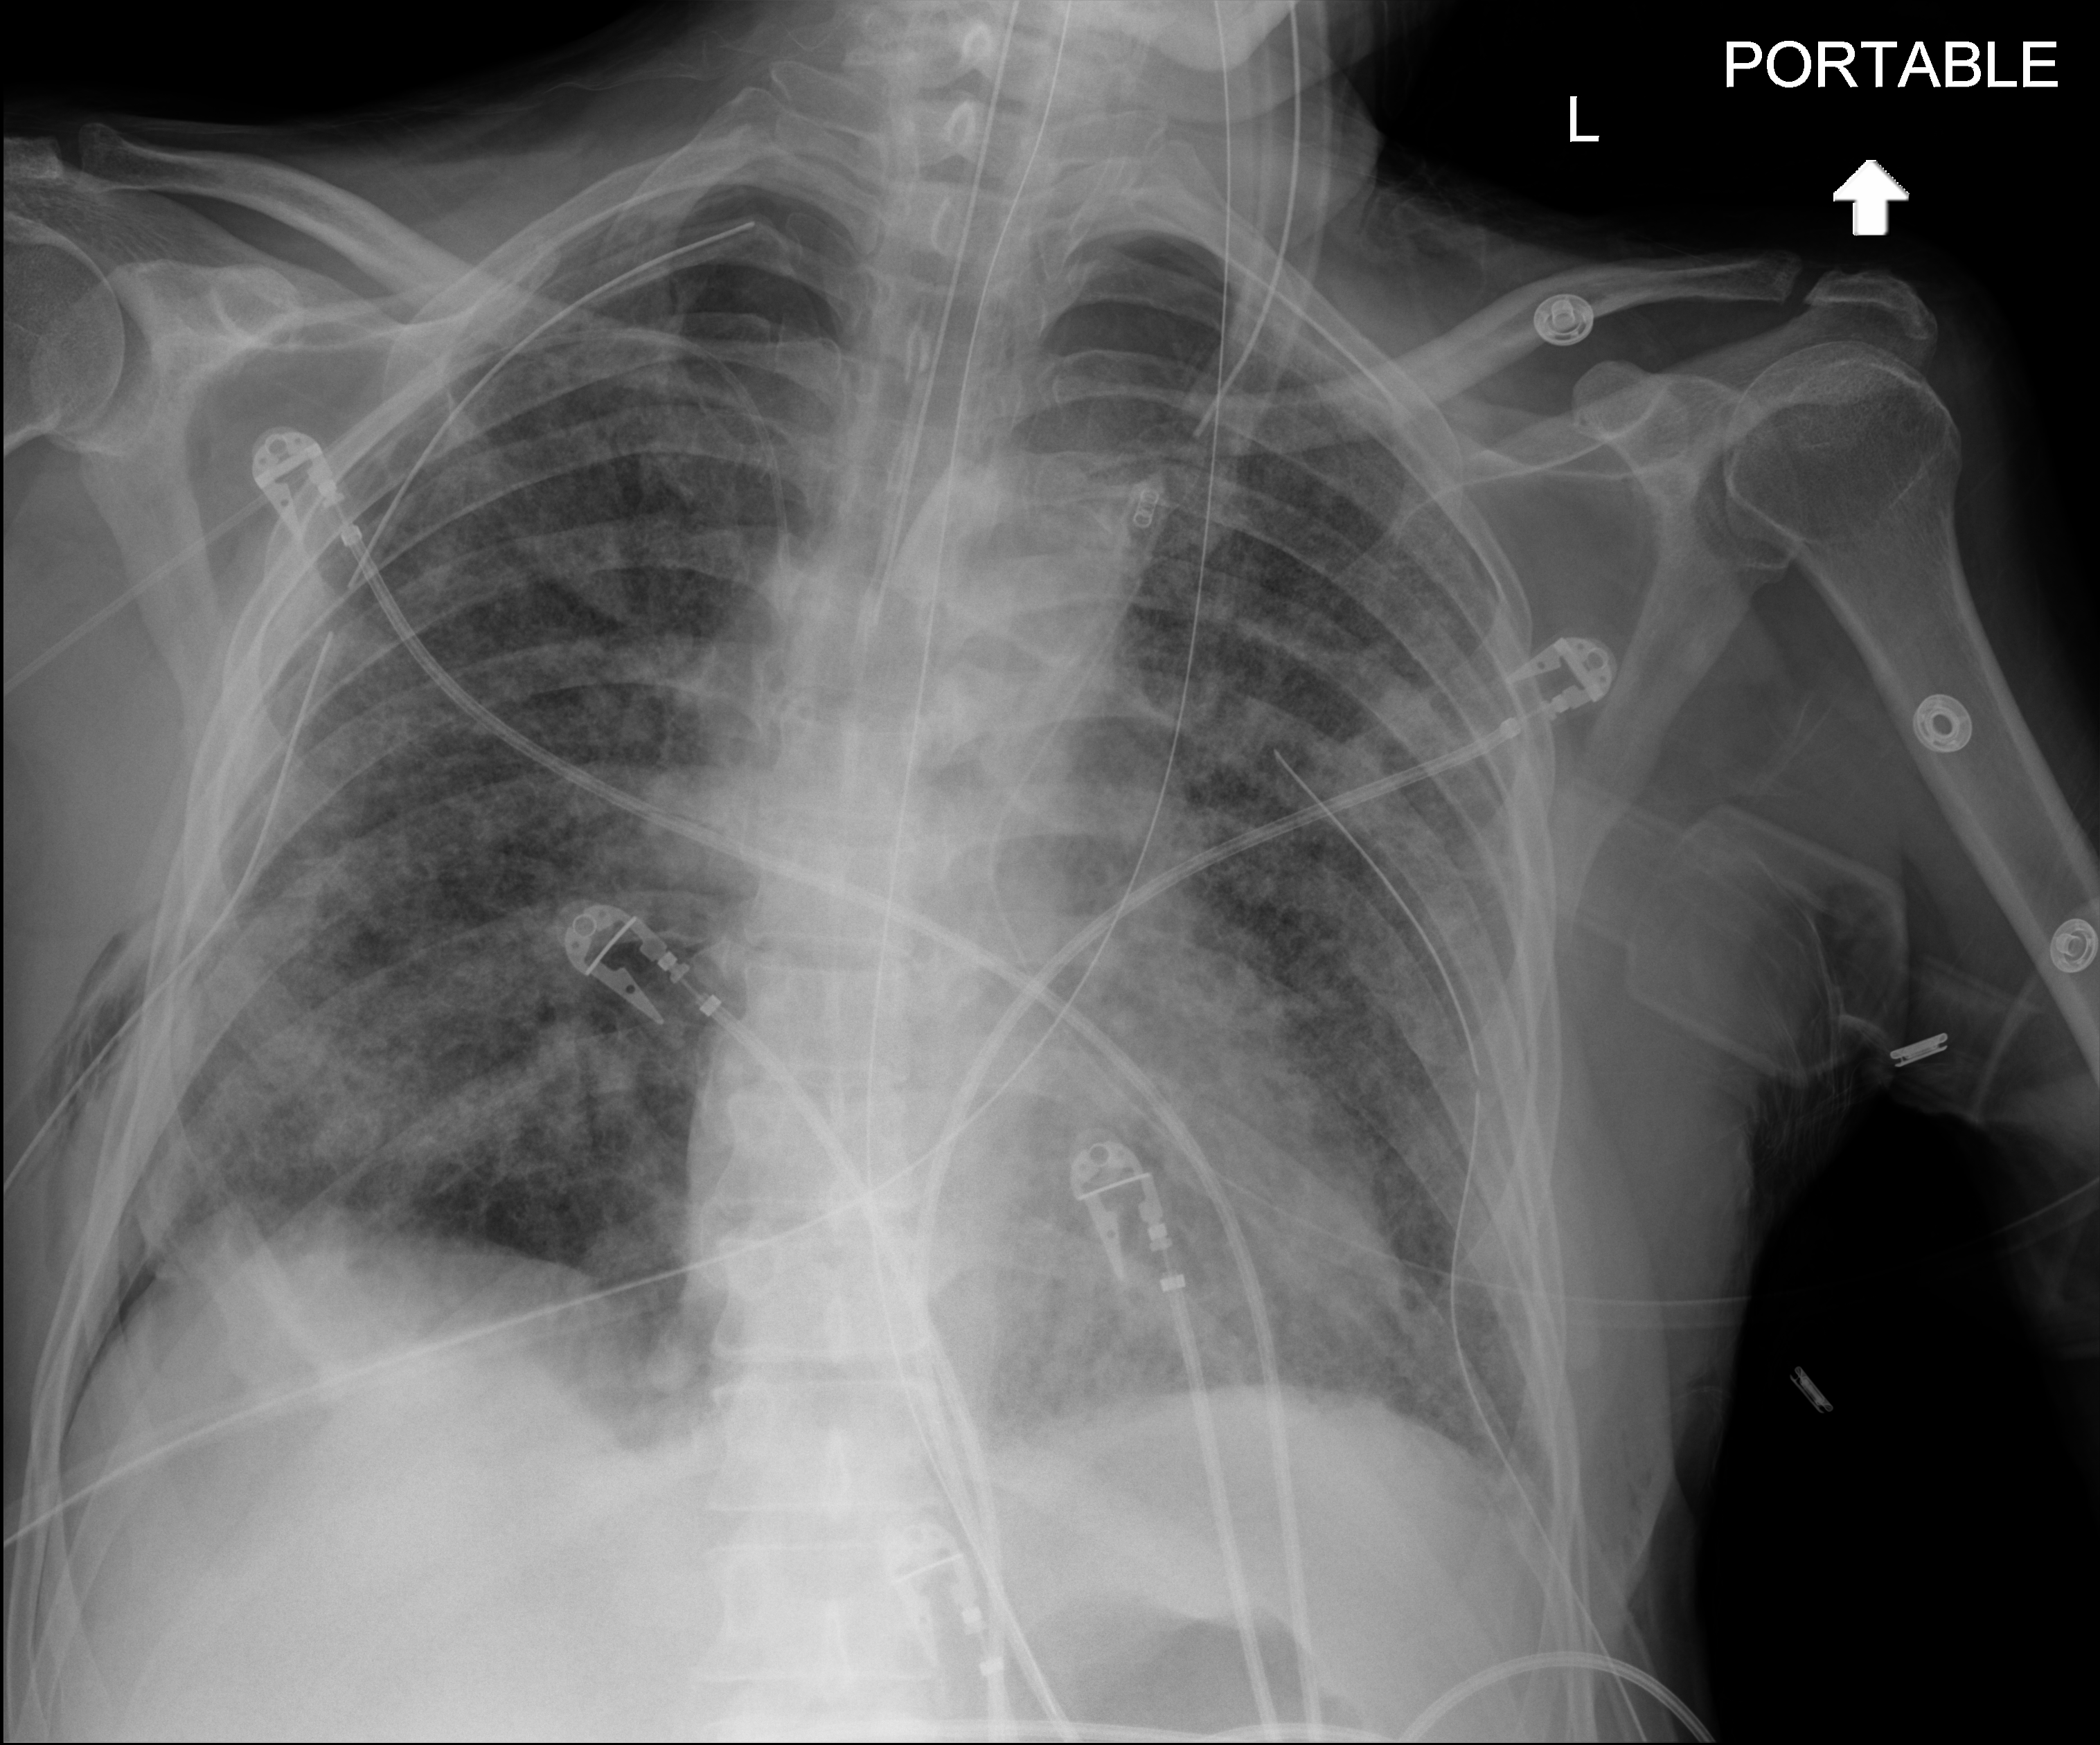
Bedside chest radiograph (digital radiography). Patient hospitalised with COVID-19; male, aged 60–74 years.
Hospital-stay facts (about this admission, not read from this image; timing relative to this image not recorded): admitted to intensive care during this hospital stay: yes; length of hospital stay: 65 days; hypertension (admission record): no.